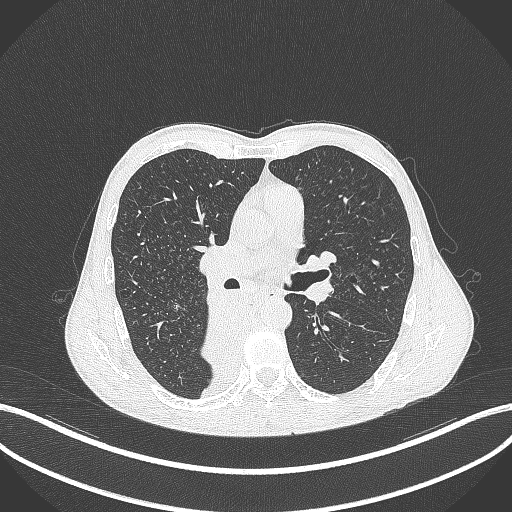
Chest CT, one axial slice; slice 216 of 371 in the series (ordered by position); lung window (W 1500 / L -600 HU); 512 × 512 image matrix, field of view 400 × 400 mm. Patient: male, 58 years. From the clinical record (not read from this slice): clinical TNM (as recorded): T3 N1 M1.
Outlined on this slice (bounding box drawn by a radiologist):
- lung tumour (recorded histology: squamous cell carcinoma): bounding box <198,297,251,380> (left, top, right, bottom; pixels)